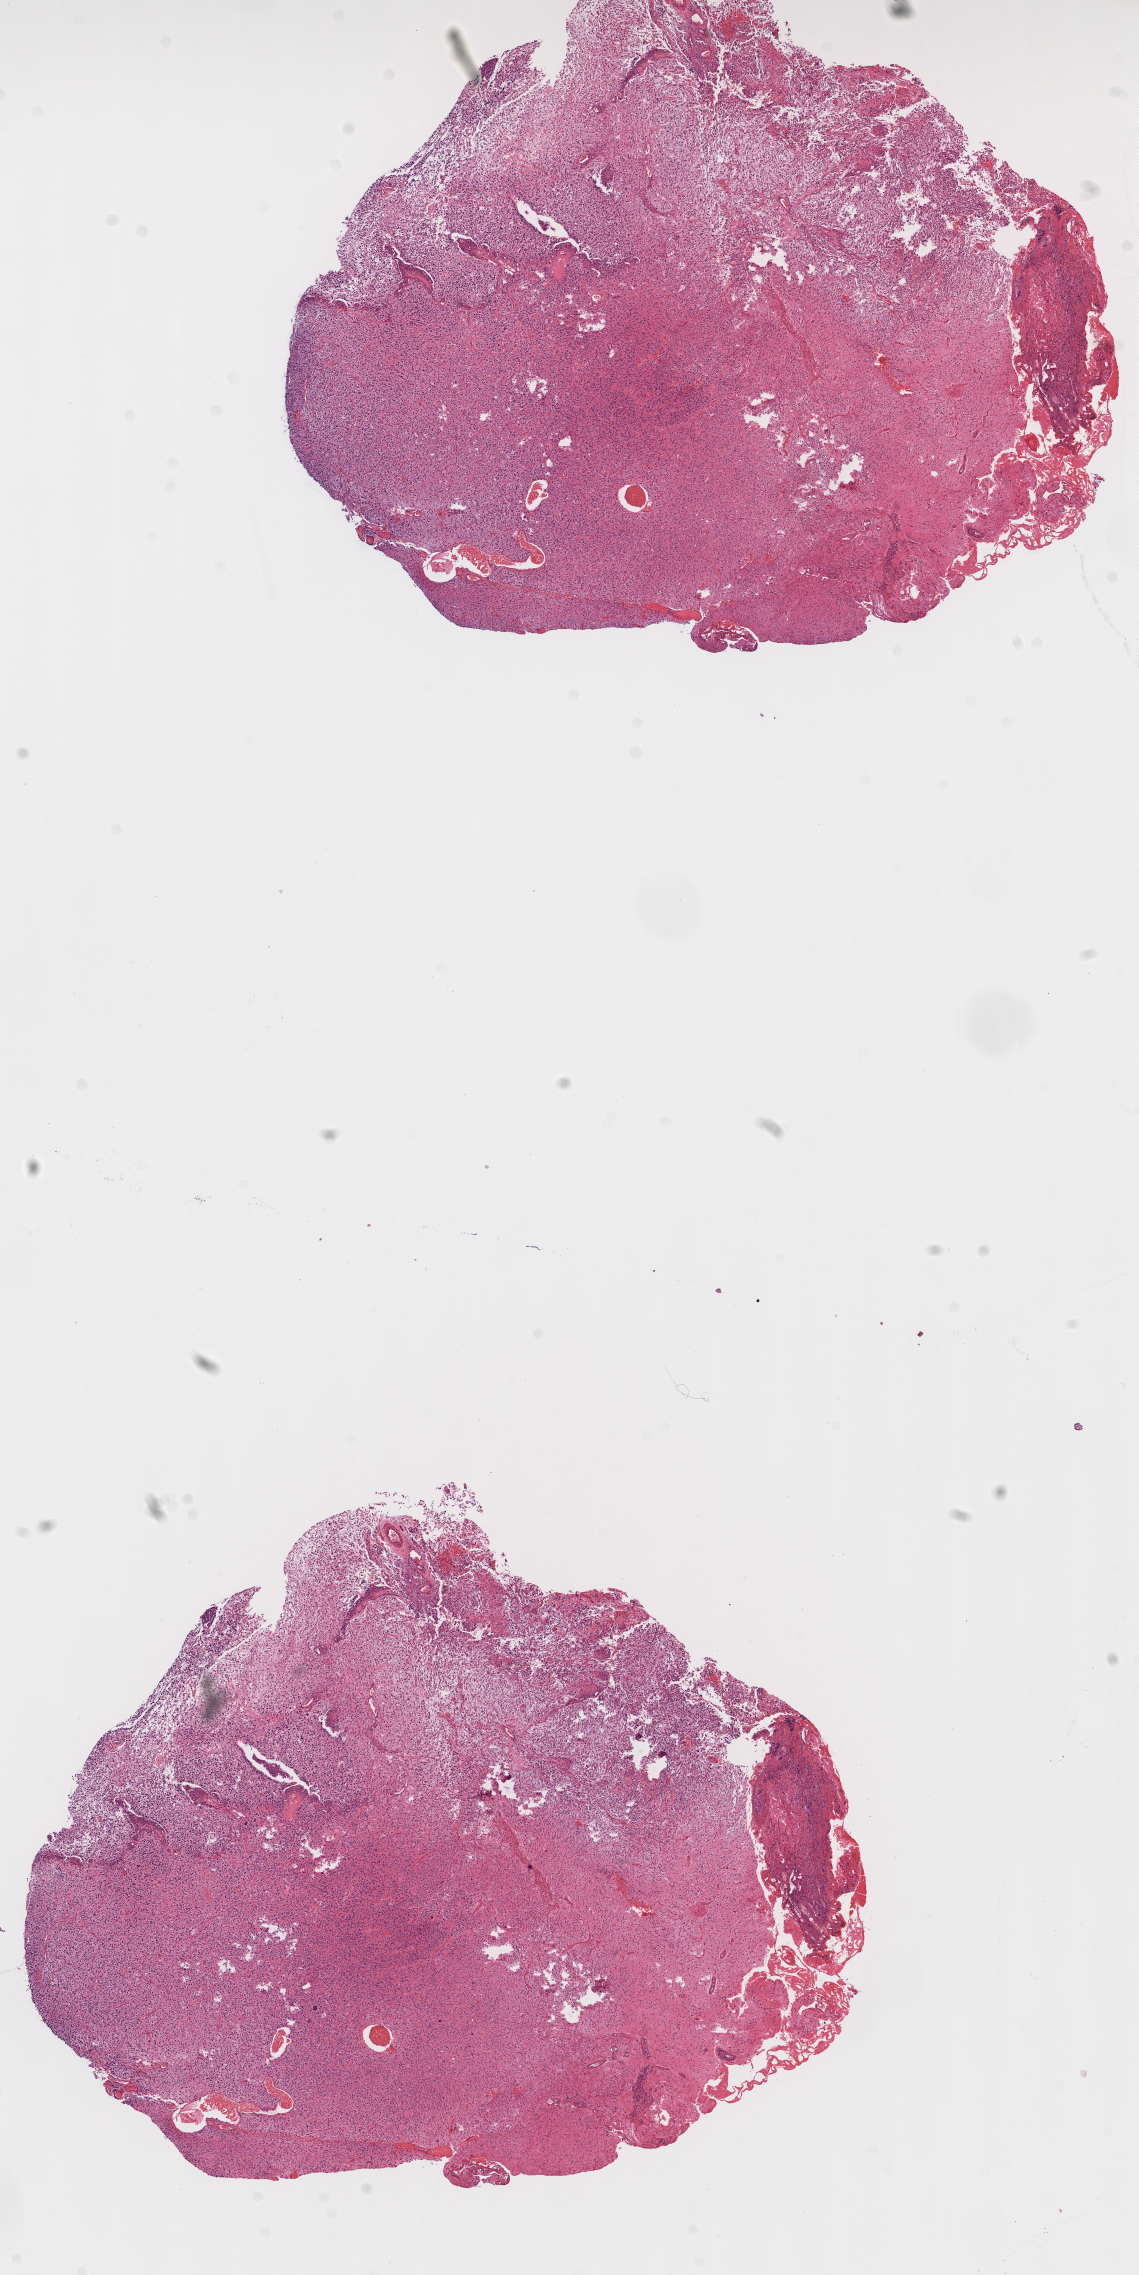
H&E-stained whole-slide image — low-resolution overview of the scanned area, about 9.2 x 18.3 mm (slide scanned at 20x). FFPE section. Sample: primary tumour, brain. Patient: male, age at initial diagnosis 66 years.
Histologic diagnosis: Glioblastoma.